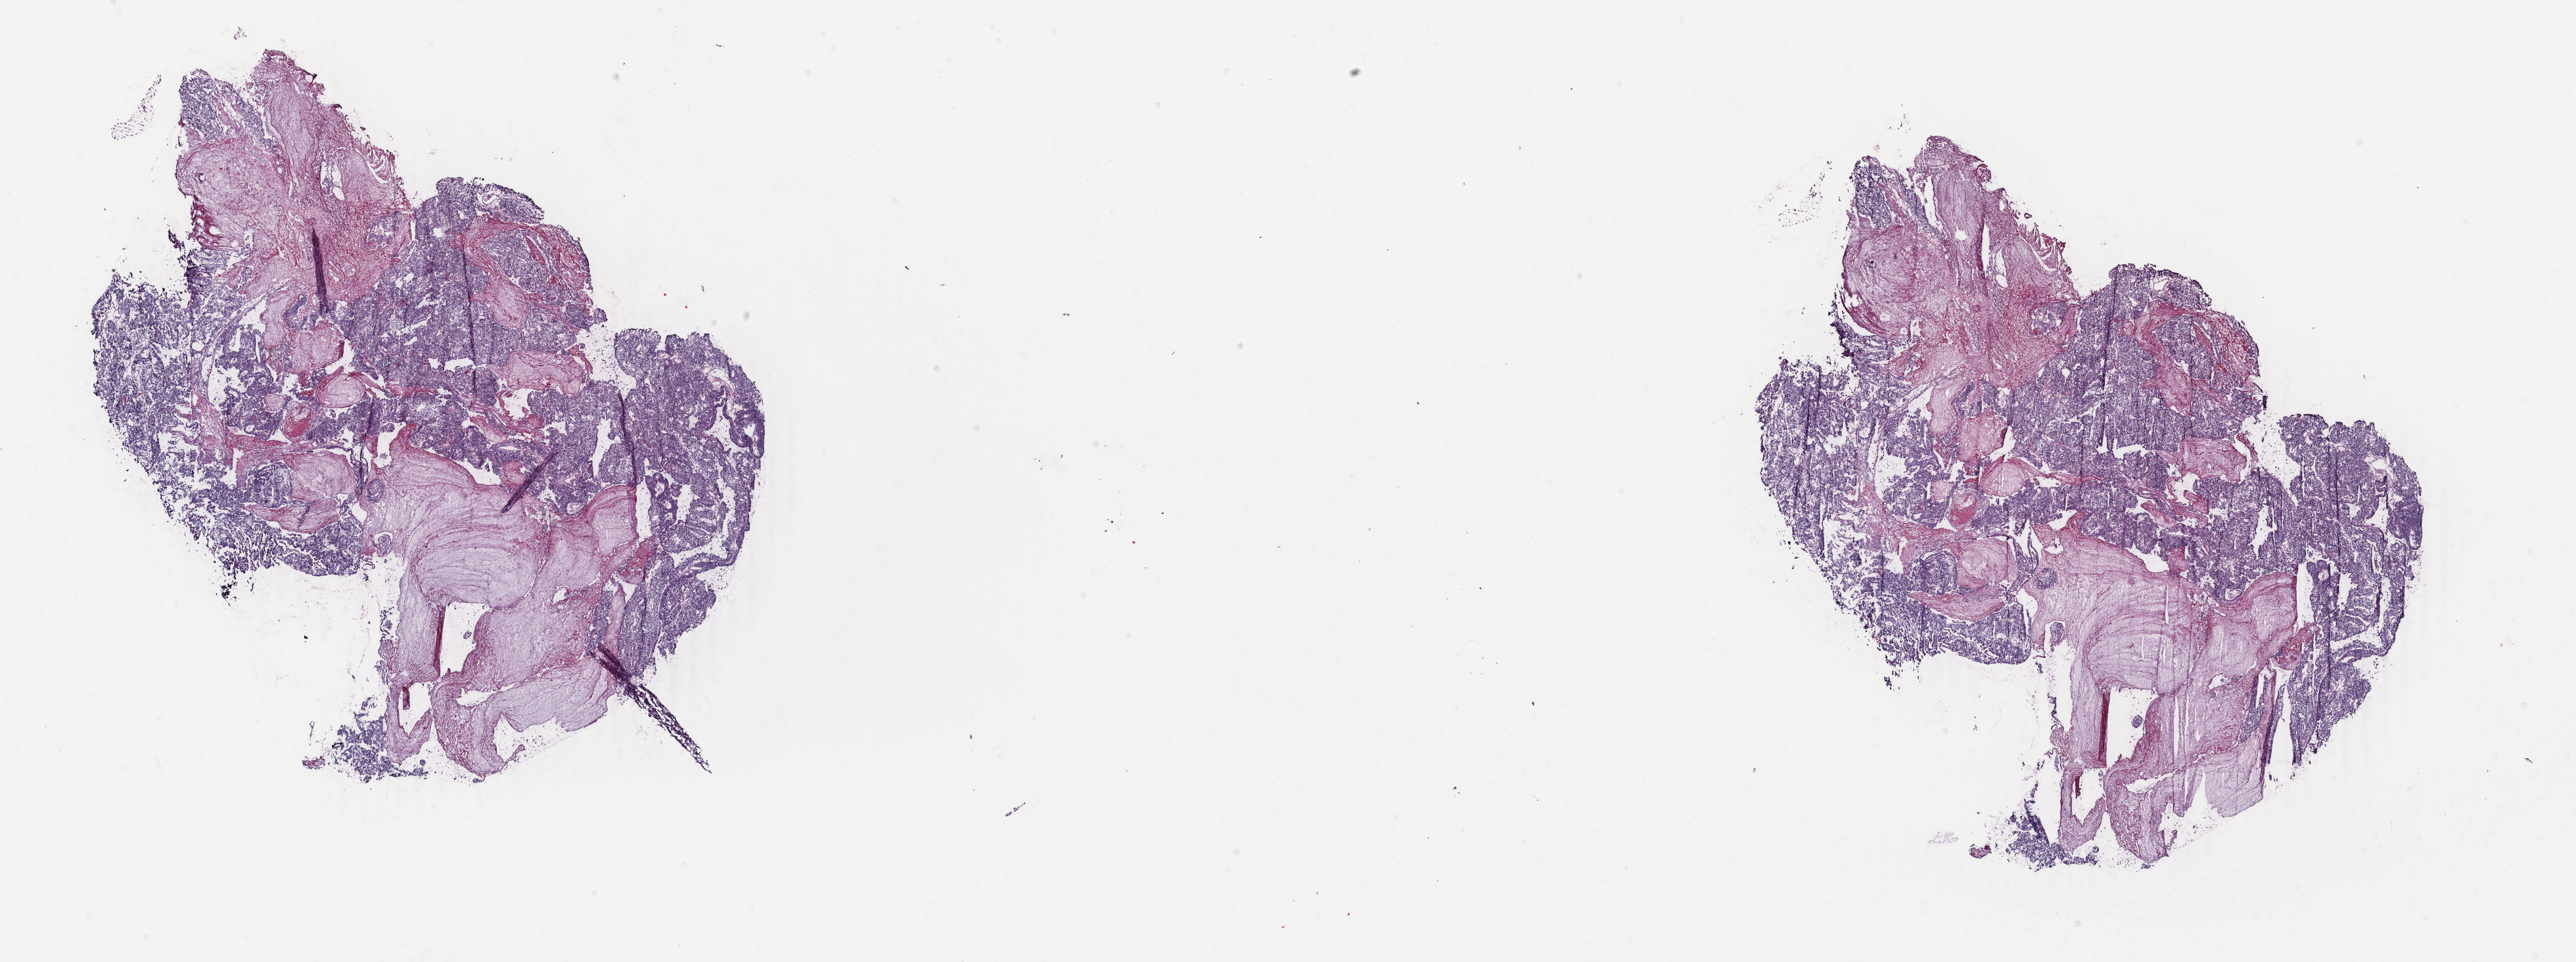
Hematoxylin and eosin (H&E) stained whole-slide image — shown as a low-resolution overview of the whole scanned area (about 31.2 x 11.6 mm). Frozen section from the top of the tissue portion. Primary tumour sample from the bladder. Male patient; age at initial diagnosis 73 years. Composition of this section per pathologist review: tumour cells 50%, tumour nuclei 80%, normal cells 0%, stromal cells 45%, necrosis 5%. Infiltration values recorded for this section: lymphocyte infiltration 0%, monocyte infiltration 0%, neutrophil infiltration 22%.
AJCC pathologic stage: I. Pathologic diagnosis: Transitional cell carcinoma (dome of bladder).